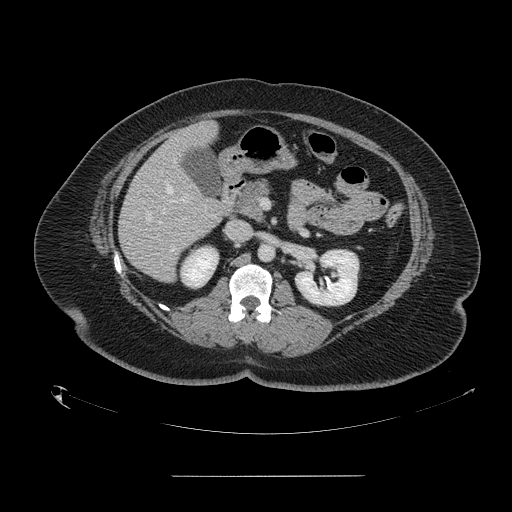
Contrast-enhanced abdominal CT, one axial slice. Slice 72 of 164 in the series (ordered by position). 120 kVp. Soft-tissue window (W 400 / L 40 HU). 2.5 mm slice thickness. 512 × 512 image matrix, field of view 495 × 495 mm. Female patient, age 52 years. From the clinical record (not read from this slice): diagnosis: colorectal cancer liver metastases, imaged before liver resection; multiple liver metastases: yes; largest metastasis: 3.5 cm.
Annotated regions visible in this slice (expert manual segmentation):
- hepatic veins: bounding box (x1, y1, x2, y2) in pixels: (146, 185, 172, 221)
- liver: (119, 122, 229, 281)
- planned liver remnant (the part of the liver to remain after resection): (178, 122, 218, 150)
- portal vein (with intrahepatic branches): (182, 198, 185, 201)